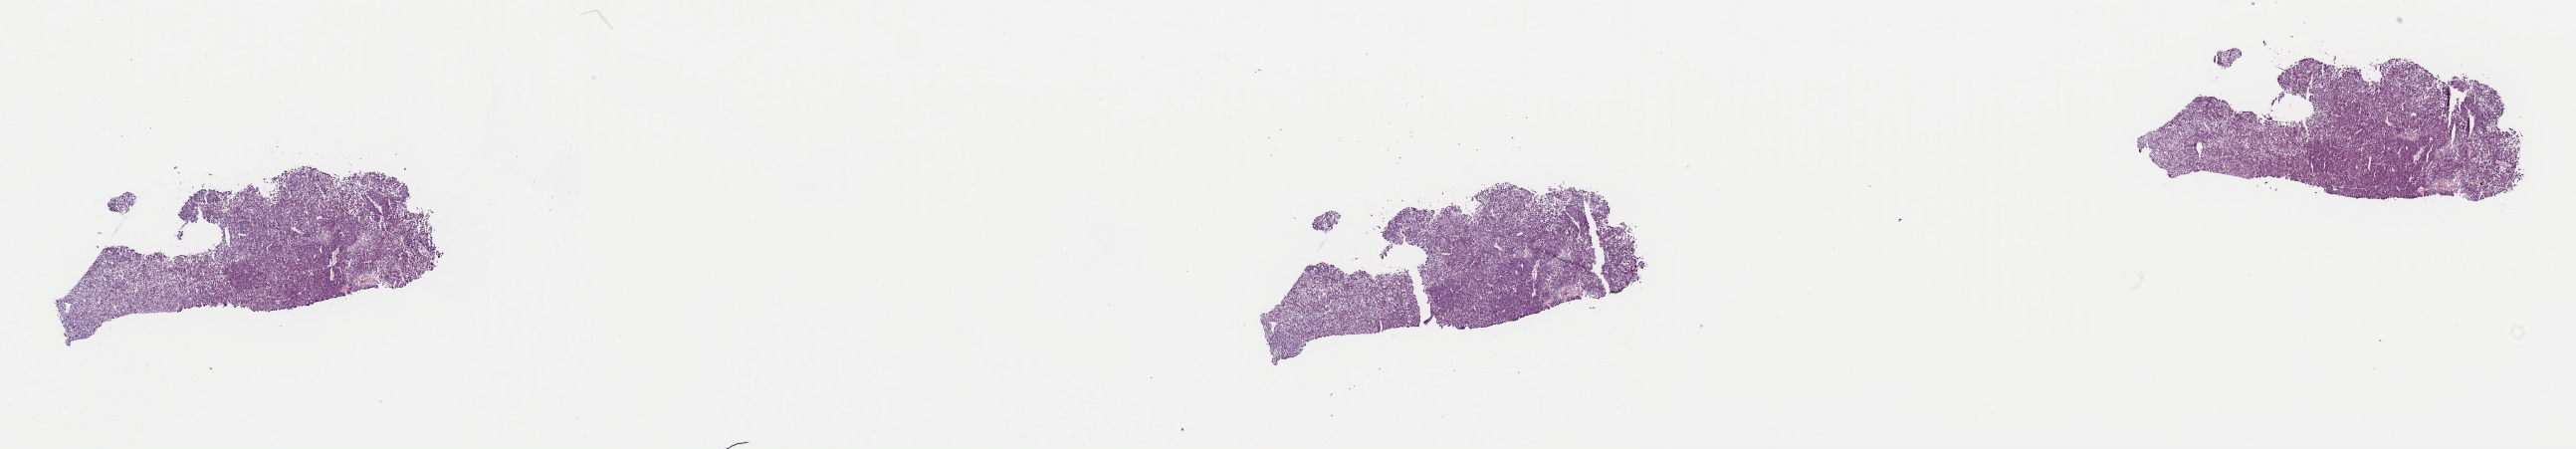
Whole-slide histology image, H&E-stained — shown as a low-resolution overview of the whole scanned area (about 40.9 x 7.1 mm). Frozen section. Sample: primary tumour, liver. Male, age 64 years at initial diagnosis. Histologic grade: G3 (poorly differentiated). Pathologist review of this section (percent, as recorded): tumour cells 93%, tumour nuclei 95%, normal cells 0%, stromal cells 5%, necrosis 2%. Infiltration values recorded for this section: lymphocyte infiltration 3%, monocyte infiltration 0%, neutrophil infiltration 0%.
- AJCC pathologic stage: I (7th edition)
- diagnosis: Hepatocellular carcinoma, NOS